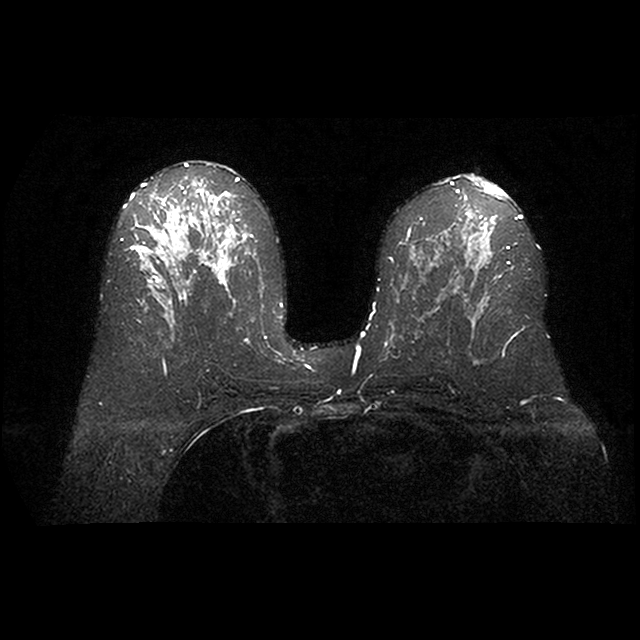
Breast MRI examination; 2 images, each one mid-volume slice chosen by position.
Image 1: axial T2-weighted / STIR image, series "STIR SENSE", slice 46 of 90, 2 mm slice thickness.
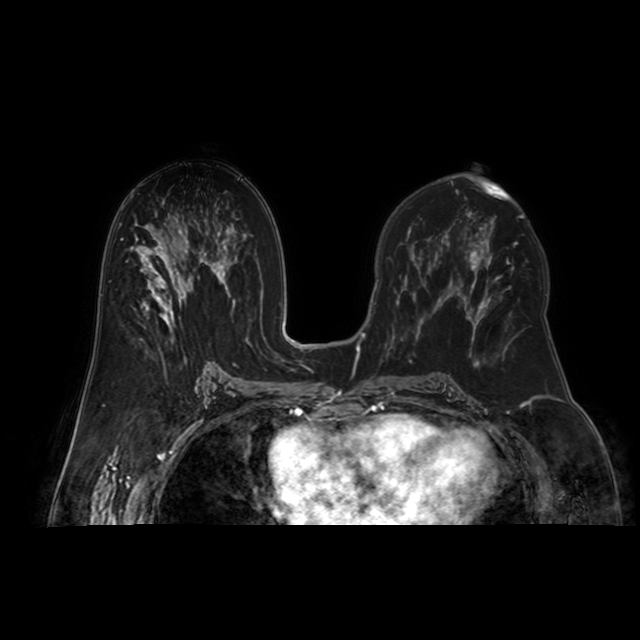
Image 2: axial dynamic contrast-enhanced T1-weighted image, series "AX BLISS_AUTO SENSE", slice 46 of 90, dynamic phase 6 of 10, 4 mm slice thickness.
Pathology recorded for this patient (not read from these images): pathology diagnosis: benign fibrosis (left breast).